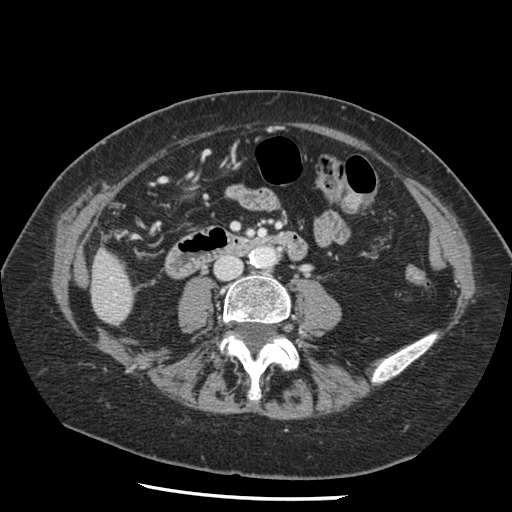
Contrast-enhanced abdominal CT, one axial slice; position 21 of 148 along the scan axis; intravenous contrast given; soft-tissue window (W 400 / L 40 HU); 2.5 mm slice thickness; 512 × 512 image matrix, field of view 330 × 330 mm. Female patient, age 85 years. Case-level facts recorded for this patient, not image findings: diagnosis: colorectal cancer liver metastases, imaged before liver resection; multiple liver metastases: no; largest metastasis: 0.9 cm; chemotherapy before resection: yes.
Annotated regions visible in this slice (expert manual segmentation):
- liver: bounding box (x1, y1, x2, y2) in pixels: (92, 252, 133, 324)
- planned liver remnant (the part of the liver to remain after resection): (92, 252, 133, 323)